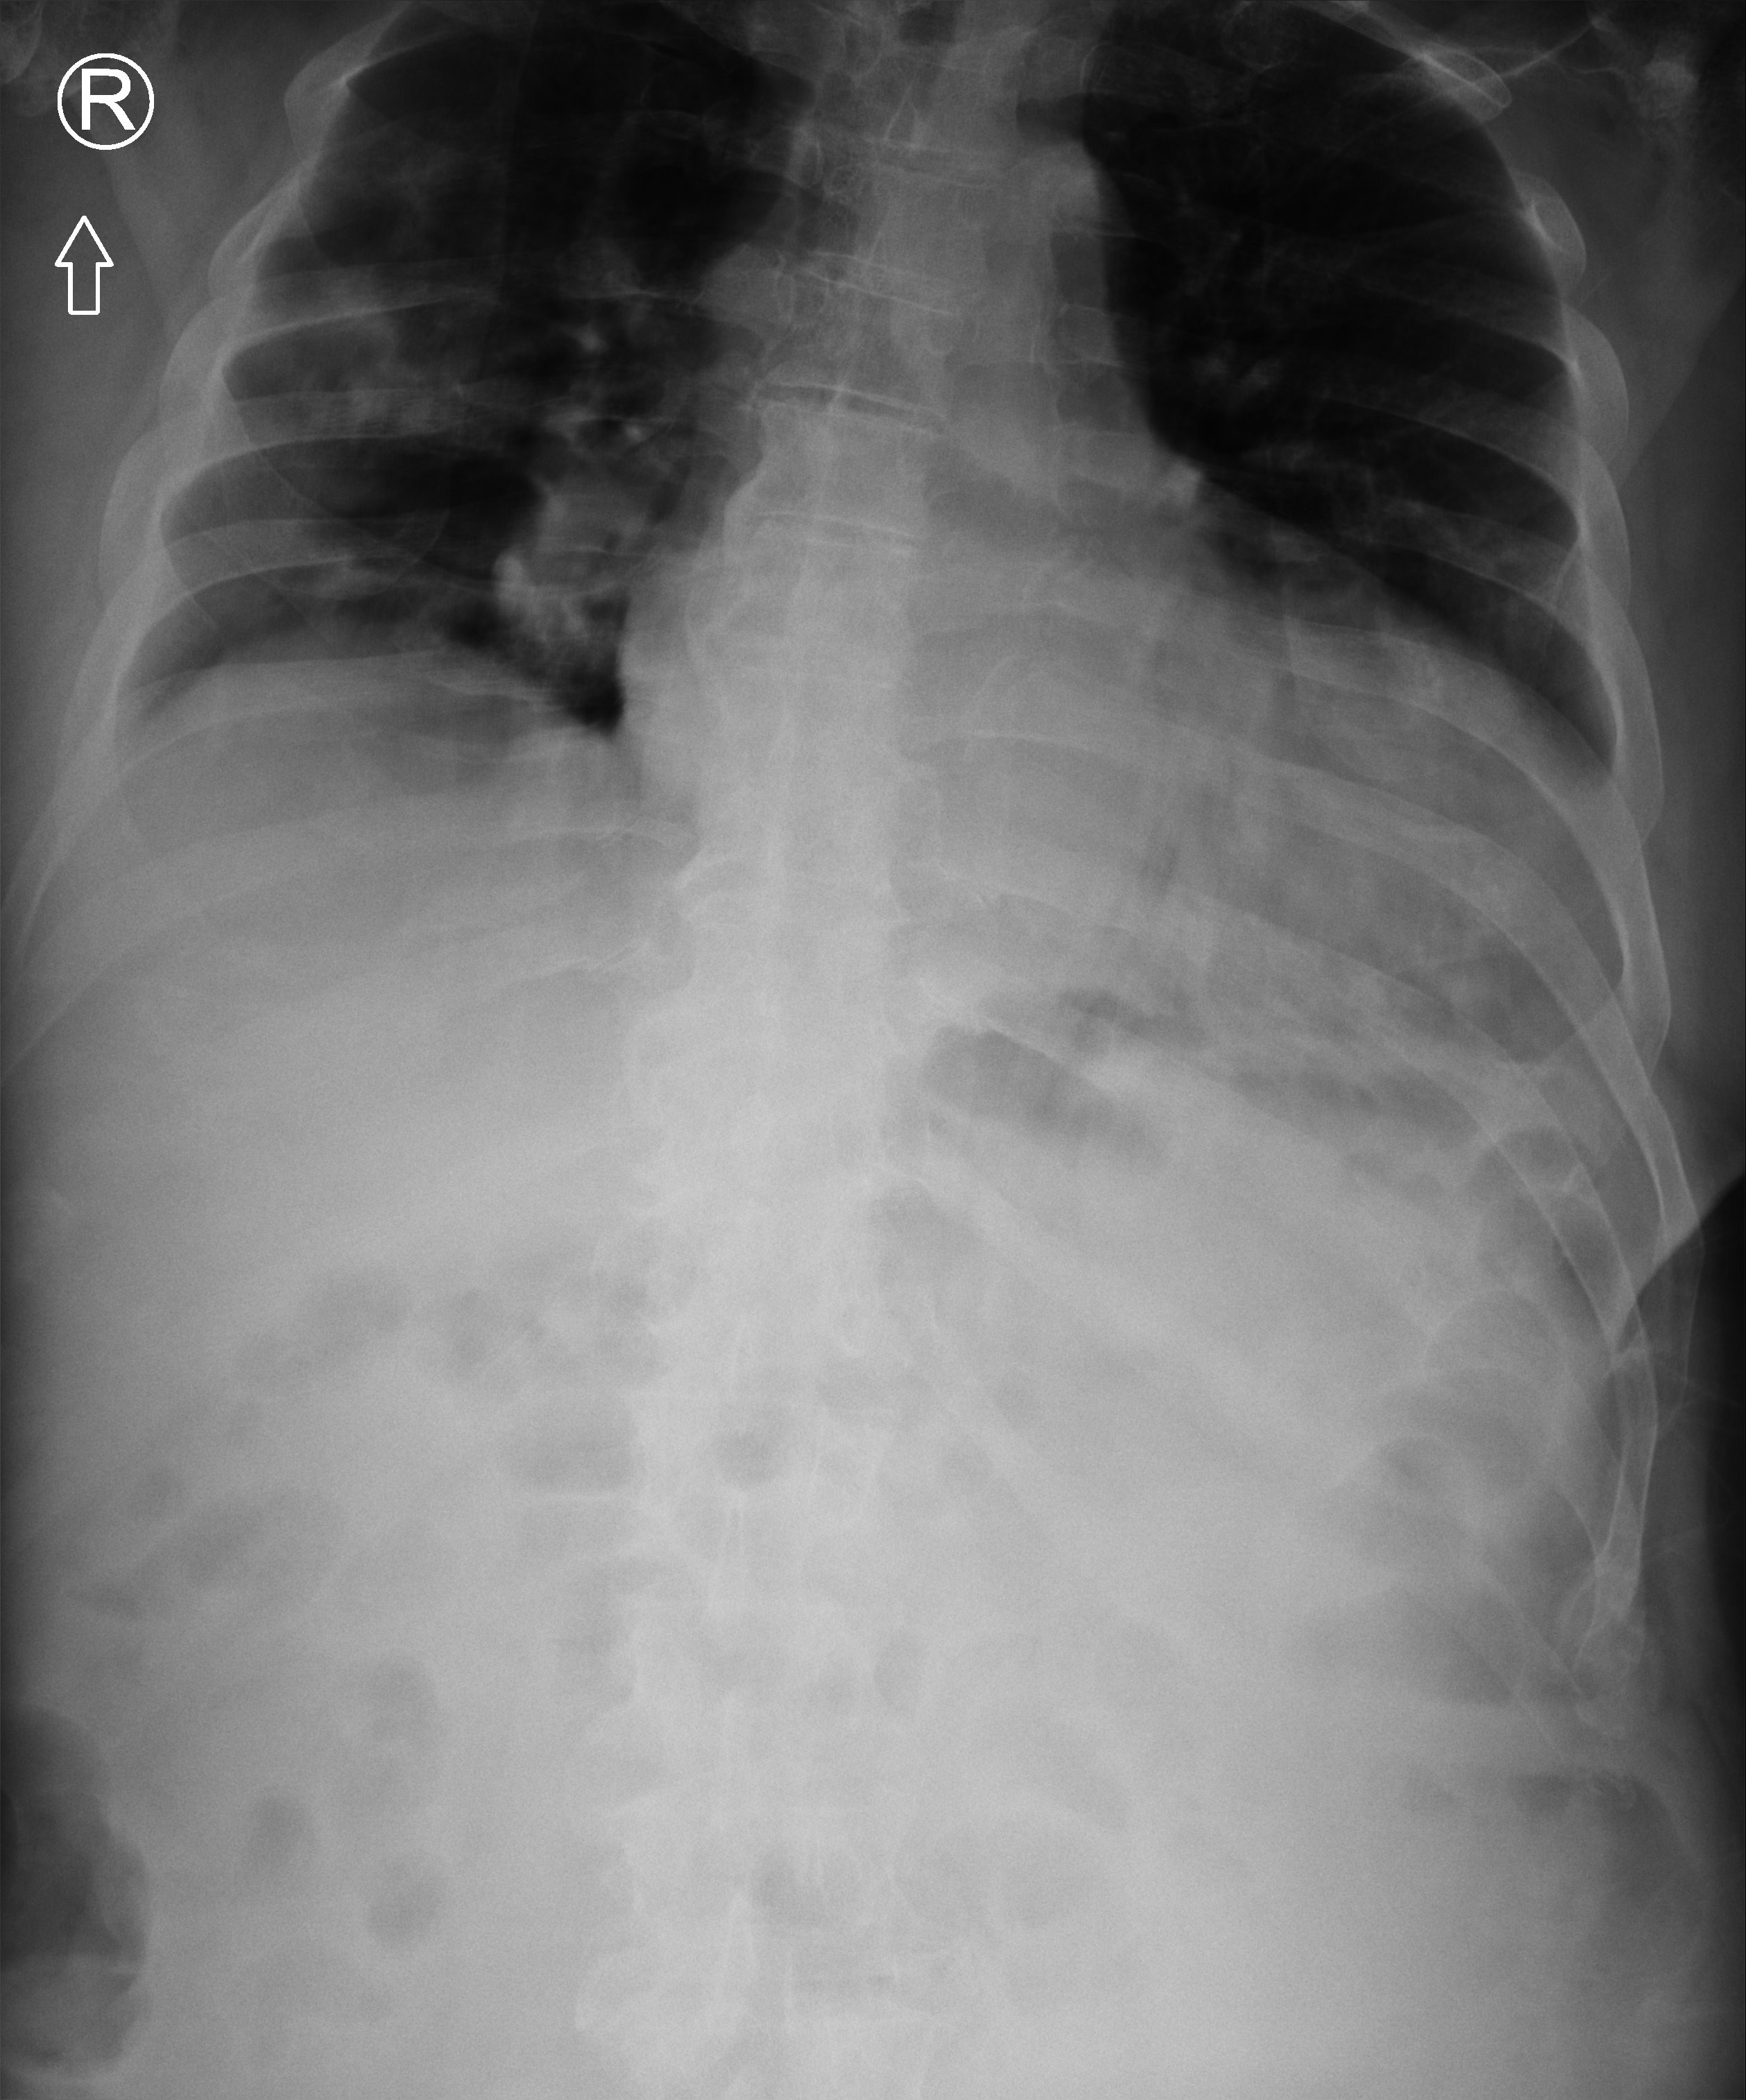
Bedside abdomen radiograph (computed radiography), anteroposterior (AP) projection. Patient hospitalised with COVID-19; male, aged 75–90 years.
Hospital-stay facts (about this admission, not read from this image; timing relative to this image not recorded): hypertension (admission record): yes; chronic kidney disease (admission record): no.